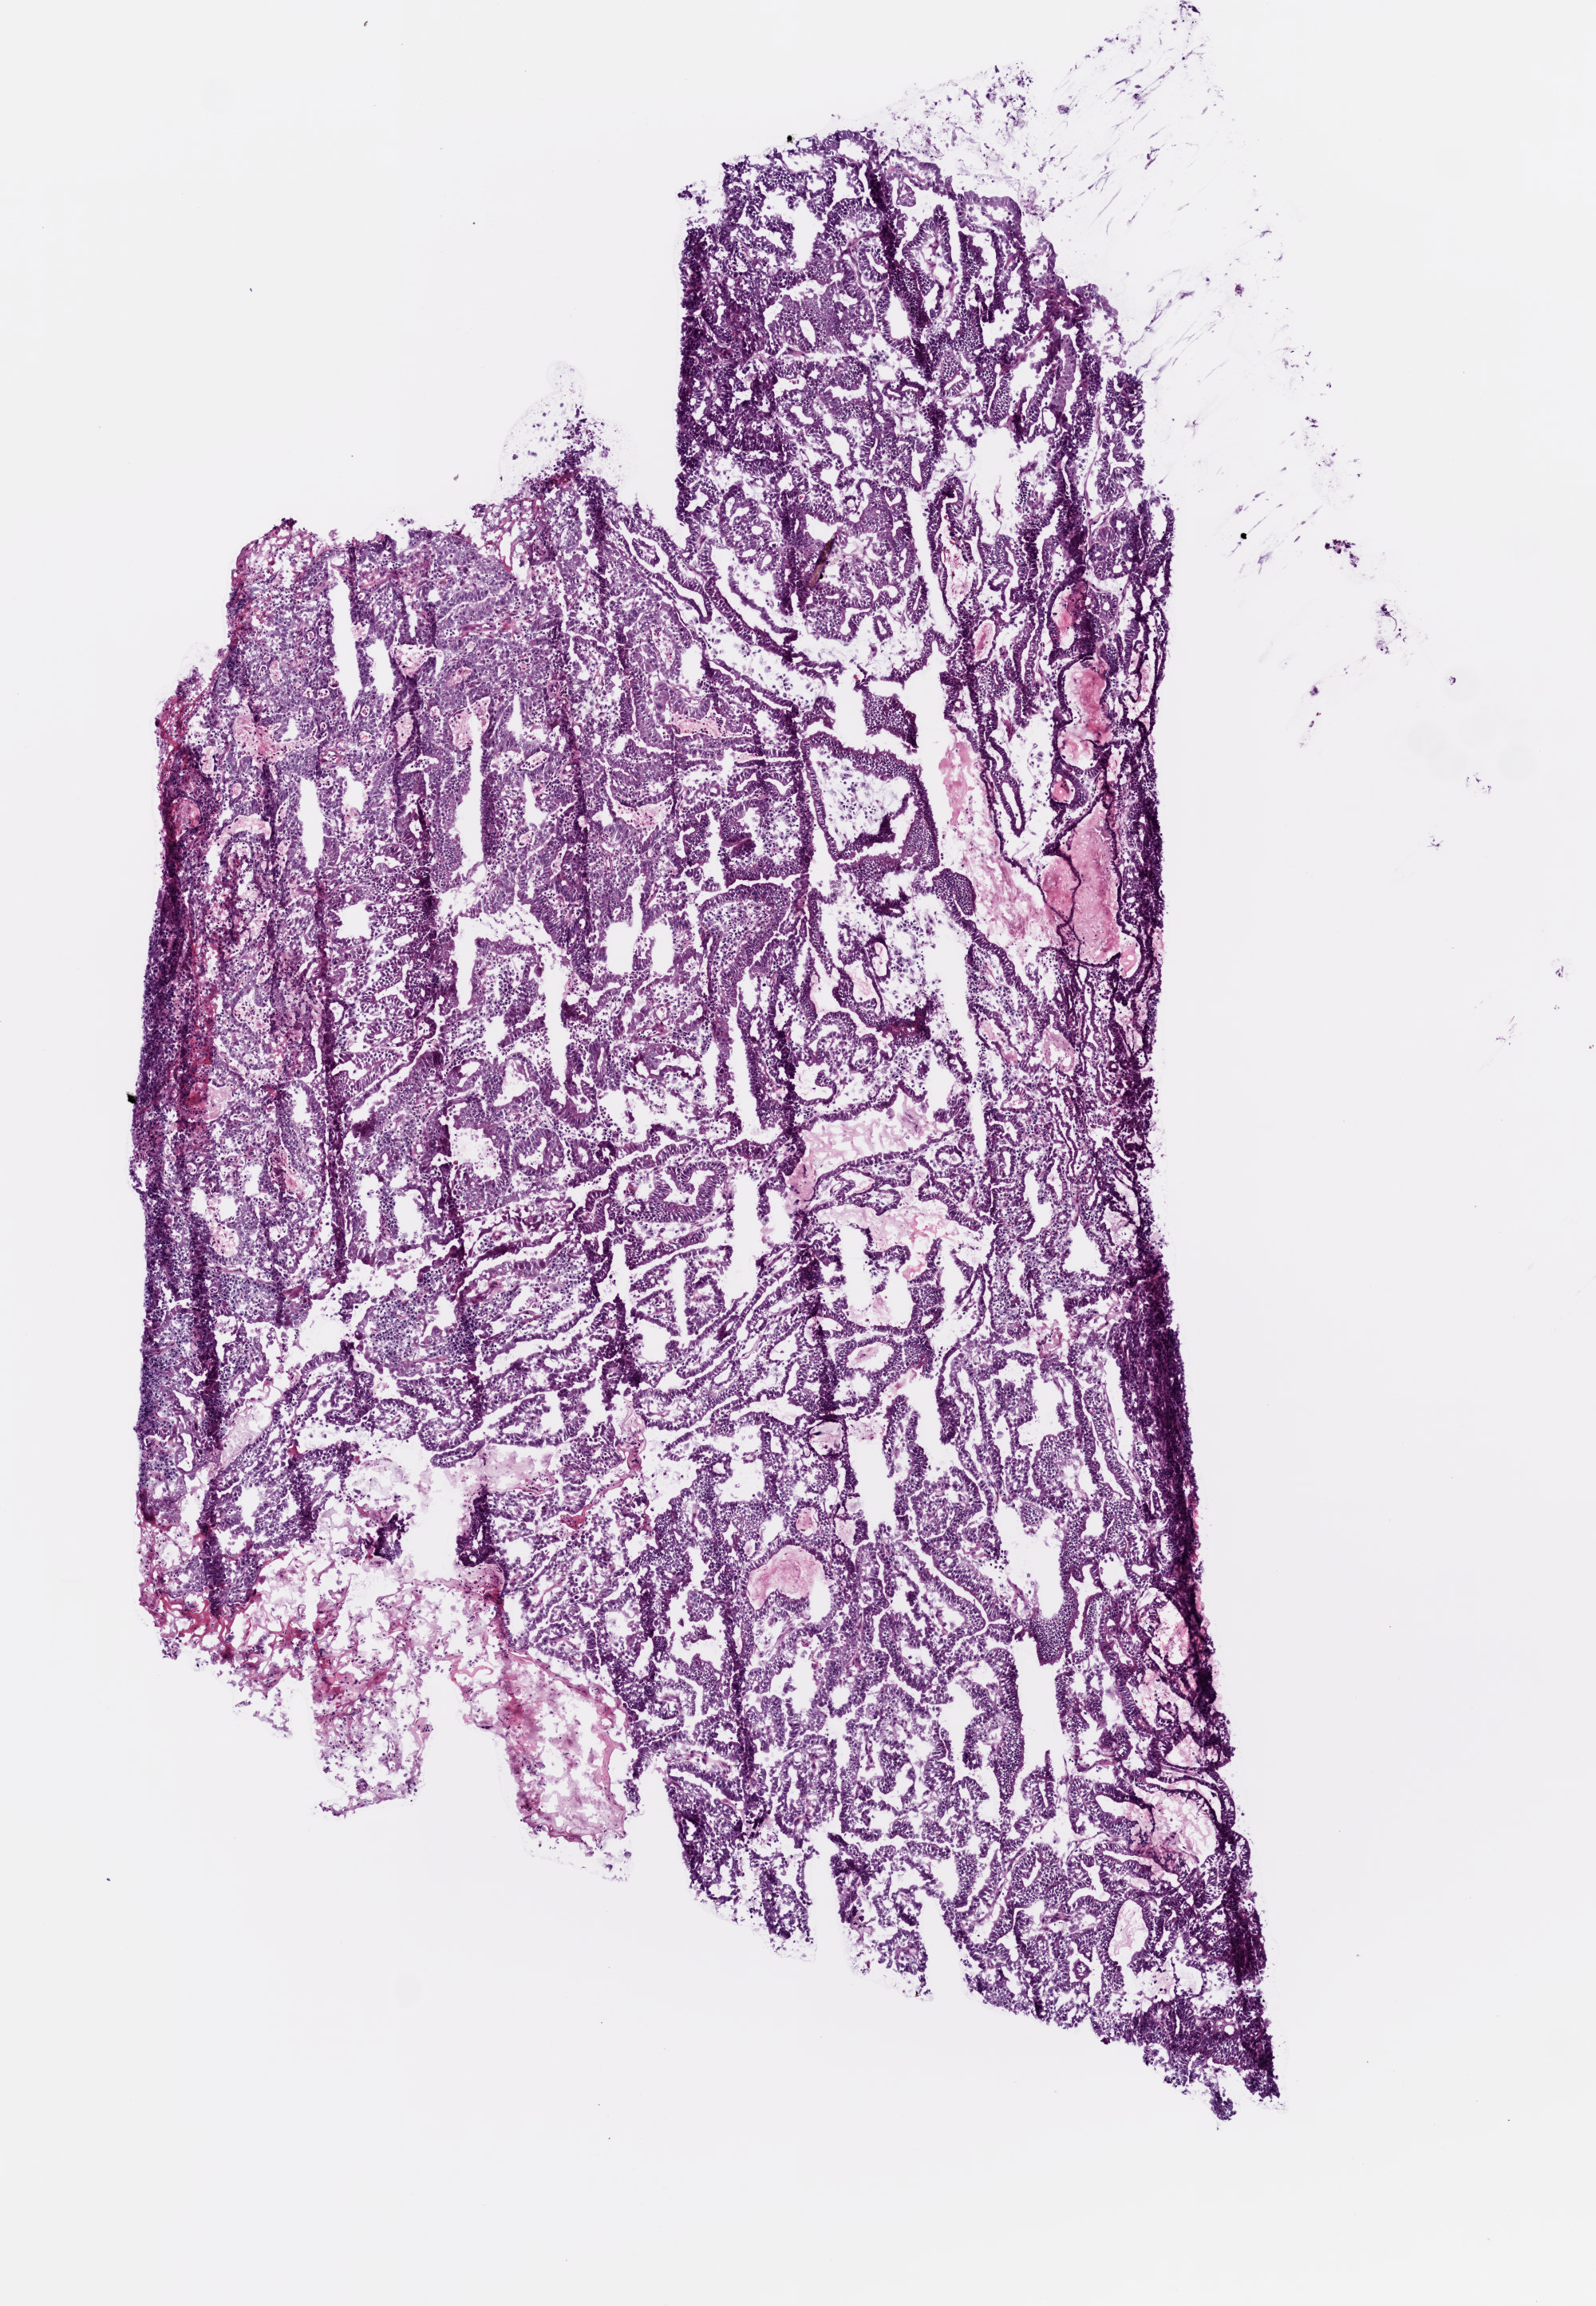
Hematoxylin and eosin (H&E) stained whole-slide image, whole scanned area (about 4.0 x 5.8 mm, from a 20x scan) shown as a low-resolution overview. Frozen section from the top of the tissue portion. Stomach, primary tumour sample. Male patient; age at initial diagnosis 66 years. Histologic grade: G2 (moderately differentiated). Slide review estimates, as recorded: tumour cells 90%, tumour nuclei 75%, normal cells 0%, stromal cells 10%, necrosis 0%.
TNM: T2 N3 M0. Pathologic diagnosis: Adenocarcinoma, intestinal type (cardia, NOS). Lymph nodes positive (case pathology): 17 of 31 examined. AJCC pathologic stage: IV (5th edition).